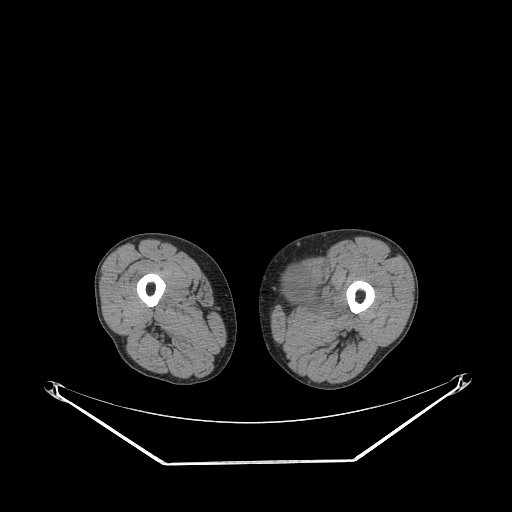
CT of an extremity soft-tissue mass (from a PET/CT study), one axial slice; 140 kVp; soft-tissue window (W 400 / L 40 HU); 3.75 mm slice thickness; 512 × 512 image matrix. Male patient. Case-level facts recorded for this patient, not image findings: histological type: pleiomorphic liposarcoma; grade: high; site of the primary tumour: left thigh.
Outlined on this slice (expert contour drawn on MRI and transferred to this co-registered scan by the dataset authors):
- gross tumour volume including surrounding oedema: bounding box [x1, y1, x2, y2] px = [288, 269, 339, 314]
- gross tumour volume (mass): [288, 269, 314, 300]